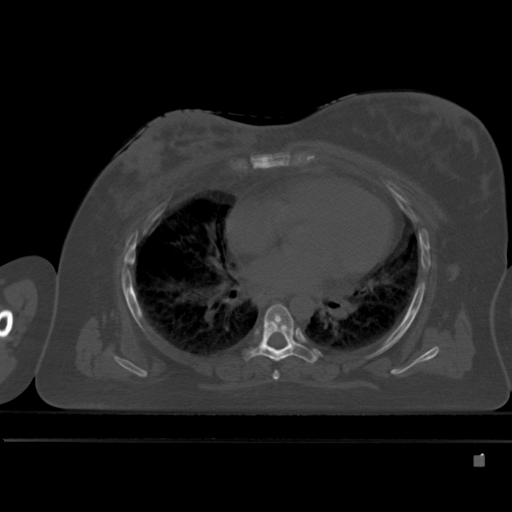
CT including the spine, one axial slice; slice 307 of 495 in the series (ordered by position); bone window (W 1800 / L 400 HU); 512 × 512 image matrix, field of view 404 × 404 mm. Patient: female, 33 years. Case-level facts recorded for this patient, not image findings: primary cancer: breast.
Annotated regions visible in this slice (semi-automatically segmented with operator editing):
- T5 vertebra: bounding box <273,371,279,380> (left, top, right, bottom; pixels)
- T6 vertebra: <246,304,319,363>